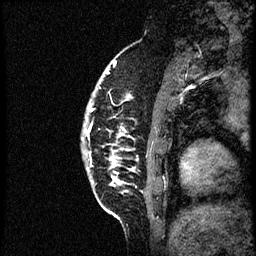
Breast MRI (dynamic contrast-enhanced), one sagittal slice. Position 11 of 56 along the scan axis. Dynamic contrast-enhanced study with each time point stored as its own series, time point 2 of 3 at this slice position (early post-contrast, ordered by acquisition time). 1.5 T. TE 4.2 ms, TR 21.3 ms. 2 mm slice thickness. 256 × 256 image matrix, field of view 200 × 200 mm. Female patient, age 41 years. Case-level facts recorded for this patient, not image findings: setting: breast cancer imaged before/during neoadjuvant chemotherapy; receptor status: HER2-positive.
Outlined on this slice (semi-automatically segmented with operator editing):
- analysis volume of interest (the breast-tissue region the enhancement analysis was run in; not a lesion): bounding box [x1, y1, x2, y2] px = [81, 73, 177, 205]
- tumour enhancement mask (voxels above the 100 % enhancement threshold inside the analysis volume of interest): [86, 76, 134, 179]